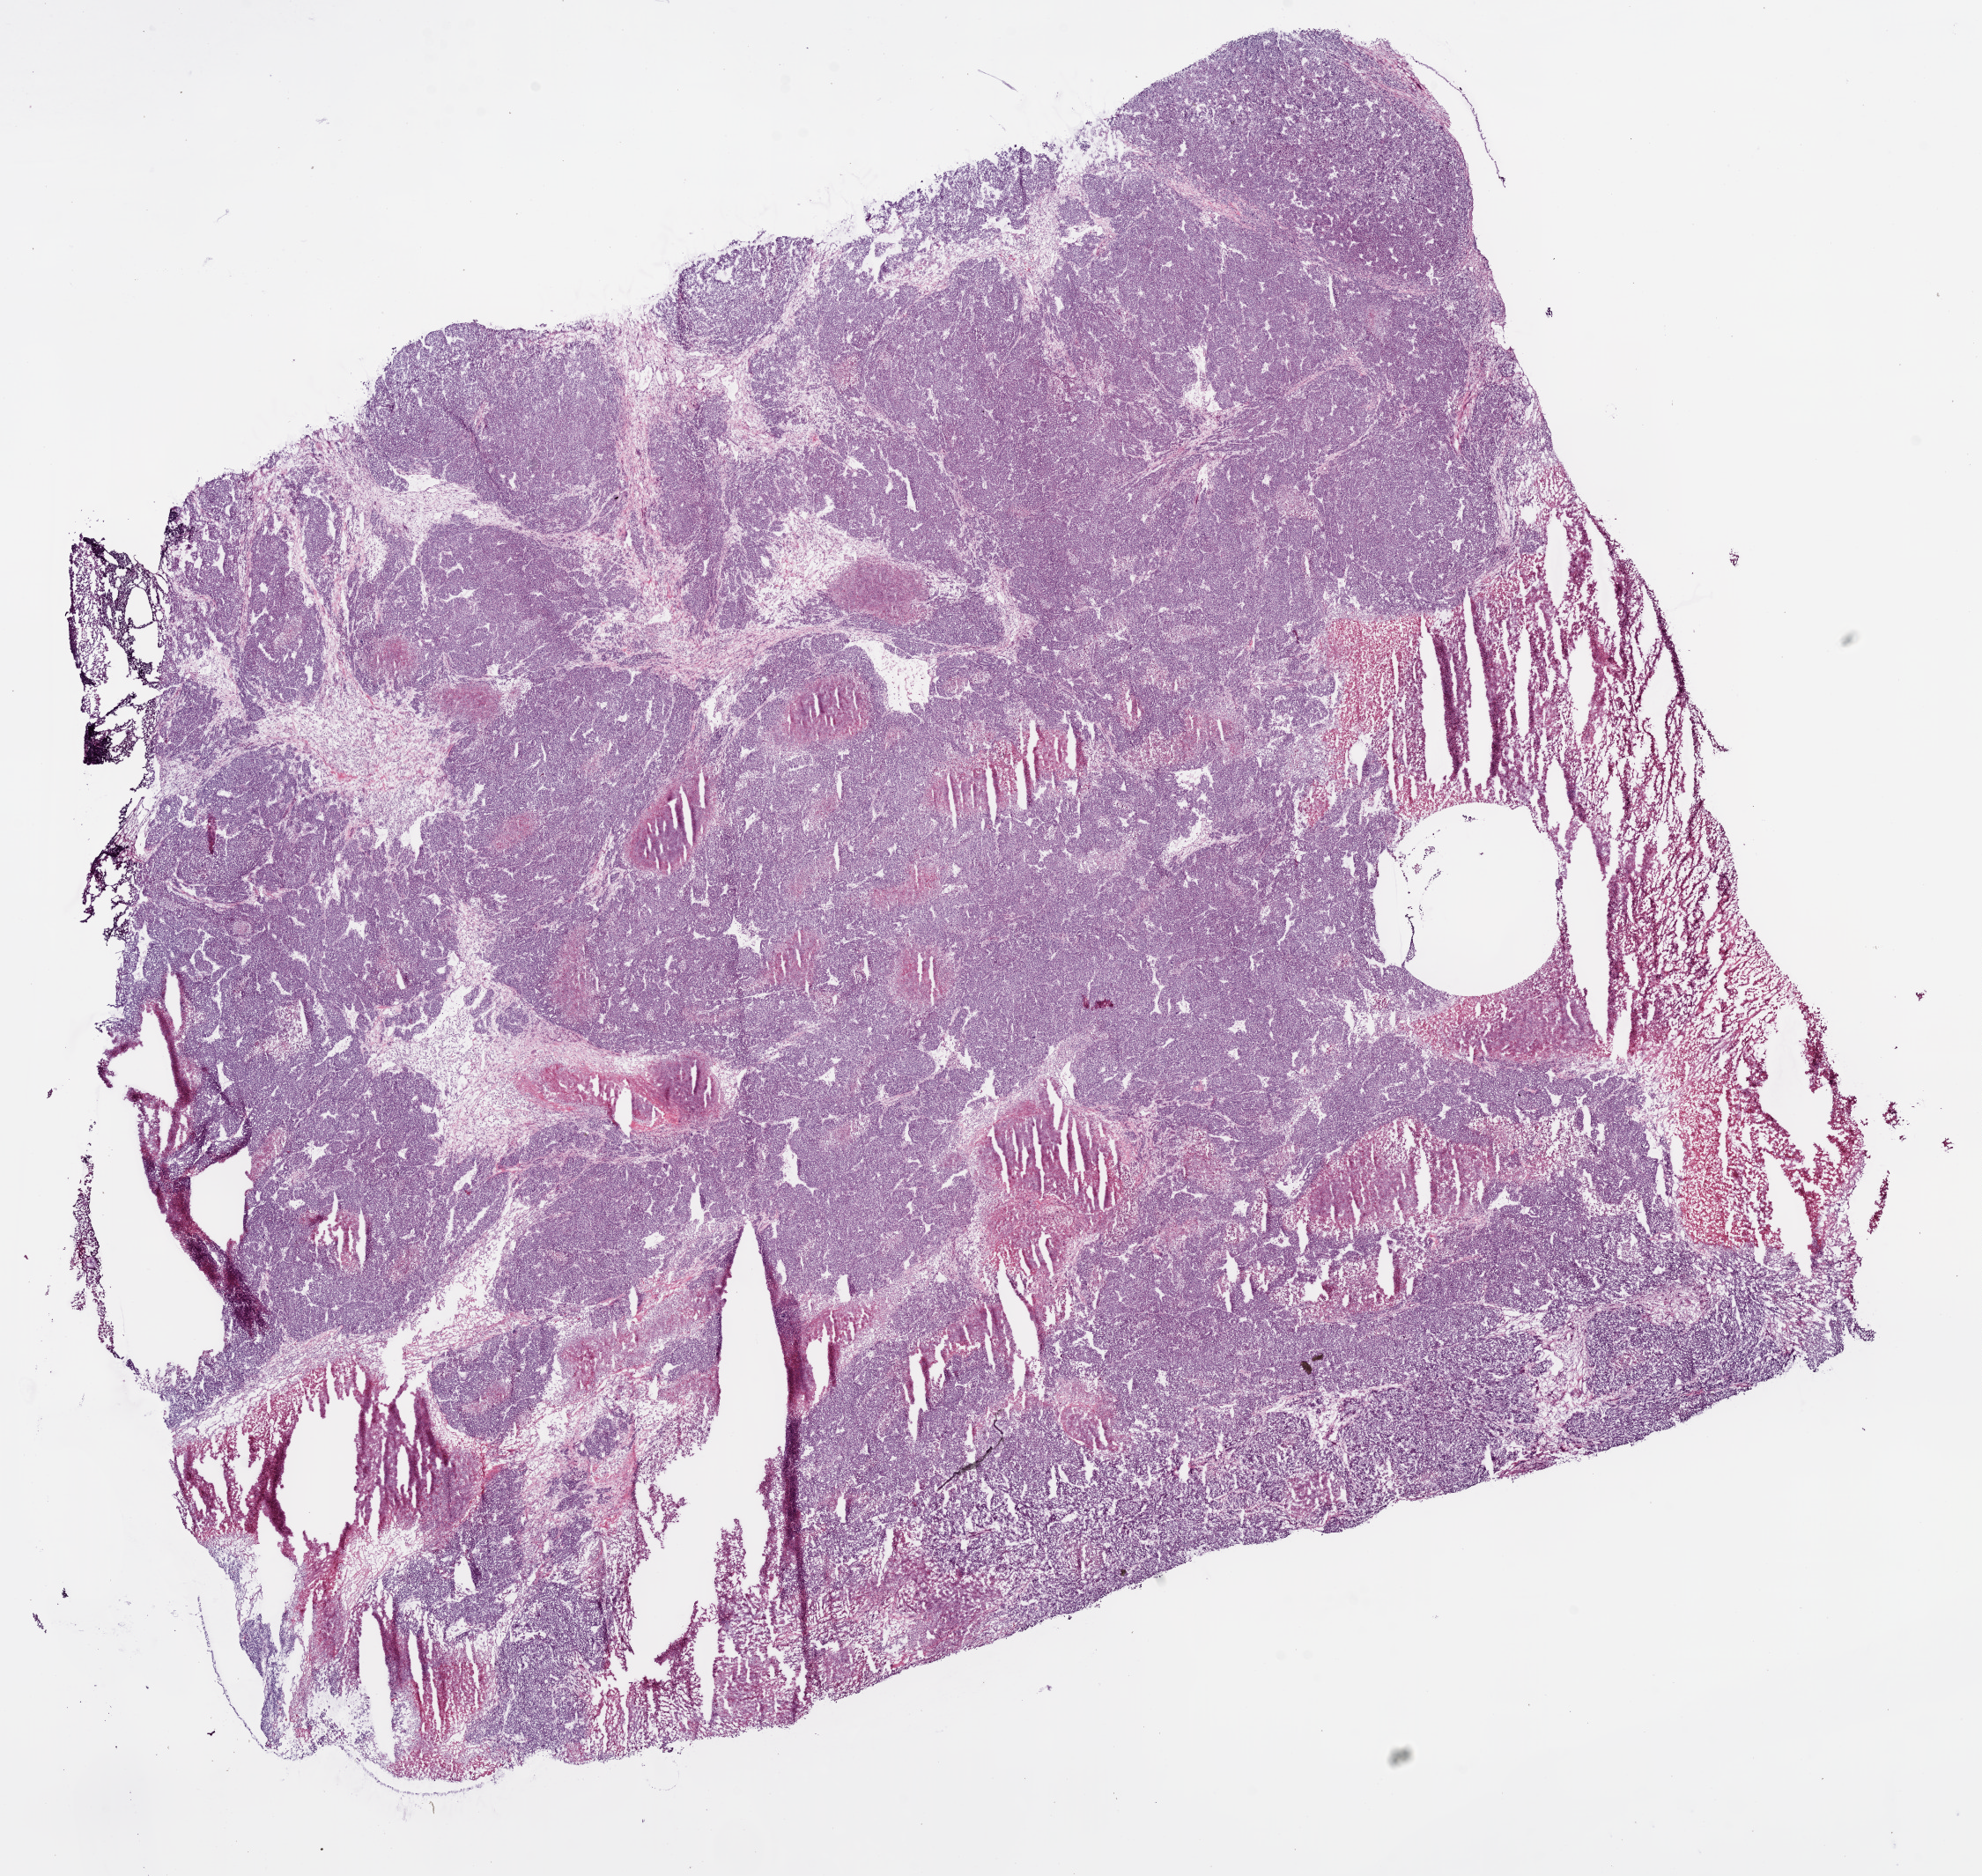
Whole-slide histology image, H&E-stained — low-resolution overview of the scanned area, about 18.1 x 17.1 mm; frozen section from the bottom of the tissue portion; primary tumour sample from the liver. Male, age 35 years at initial diagnosis. Histologic grade: G1 (well differentiated). Composition of this section per pathologist review: tumour cells 80%, tumour nuclei 85%, normal cells 0%, stromal cells 5%, necrosis 15%.
AJCC pathologic stage: IIIA (6th edition). Pathologic diagnosis: Hepatocellular carcinoma, NOS.